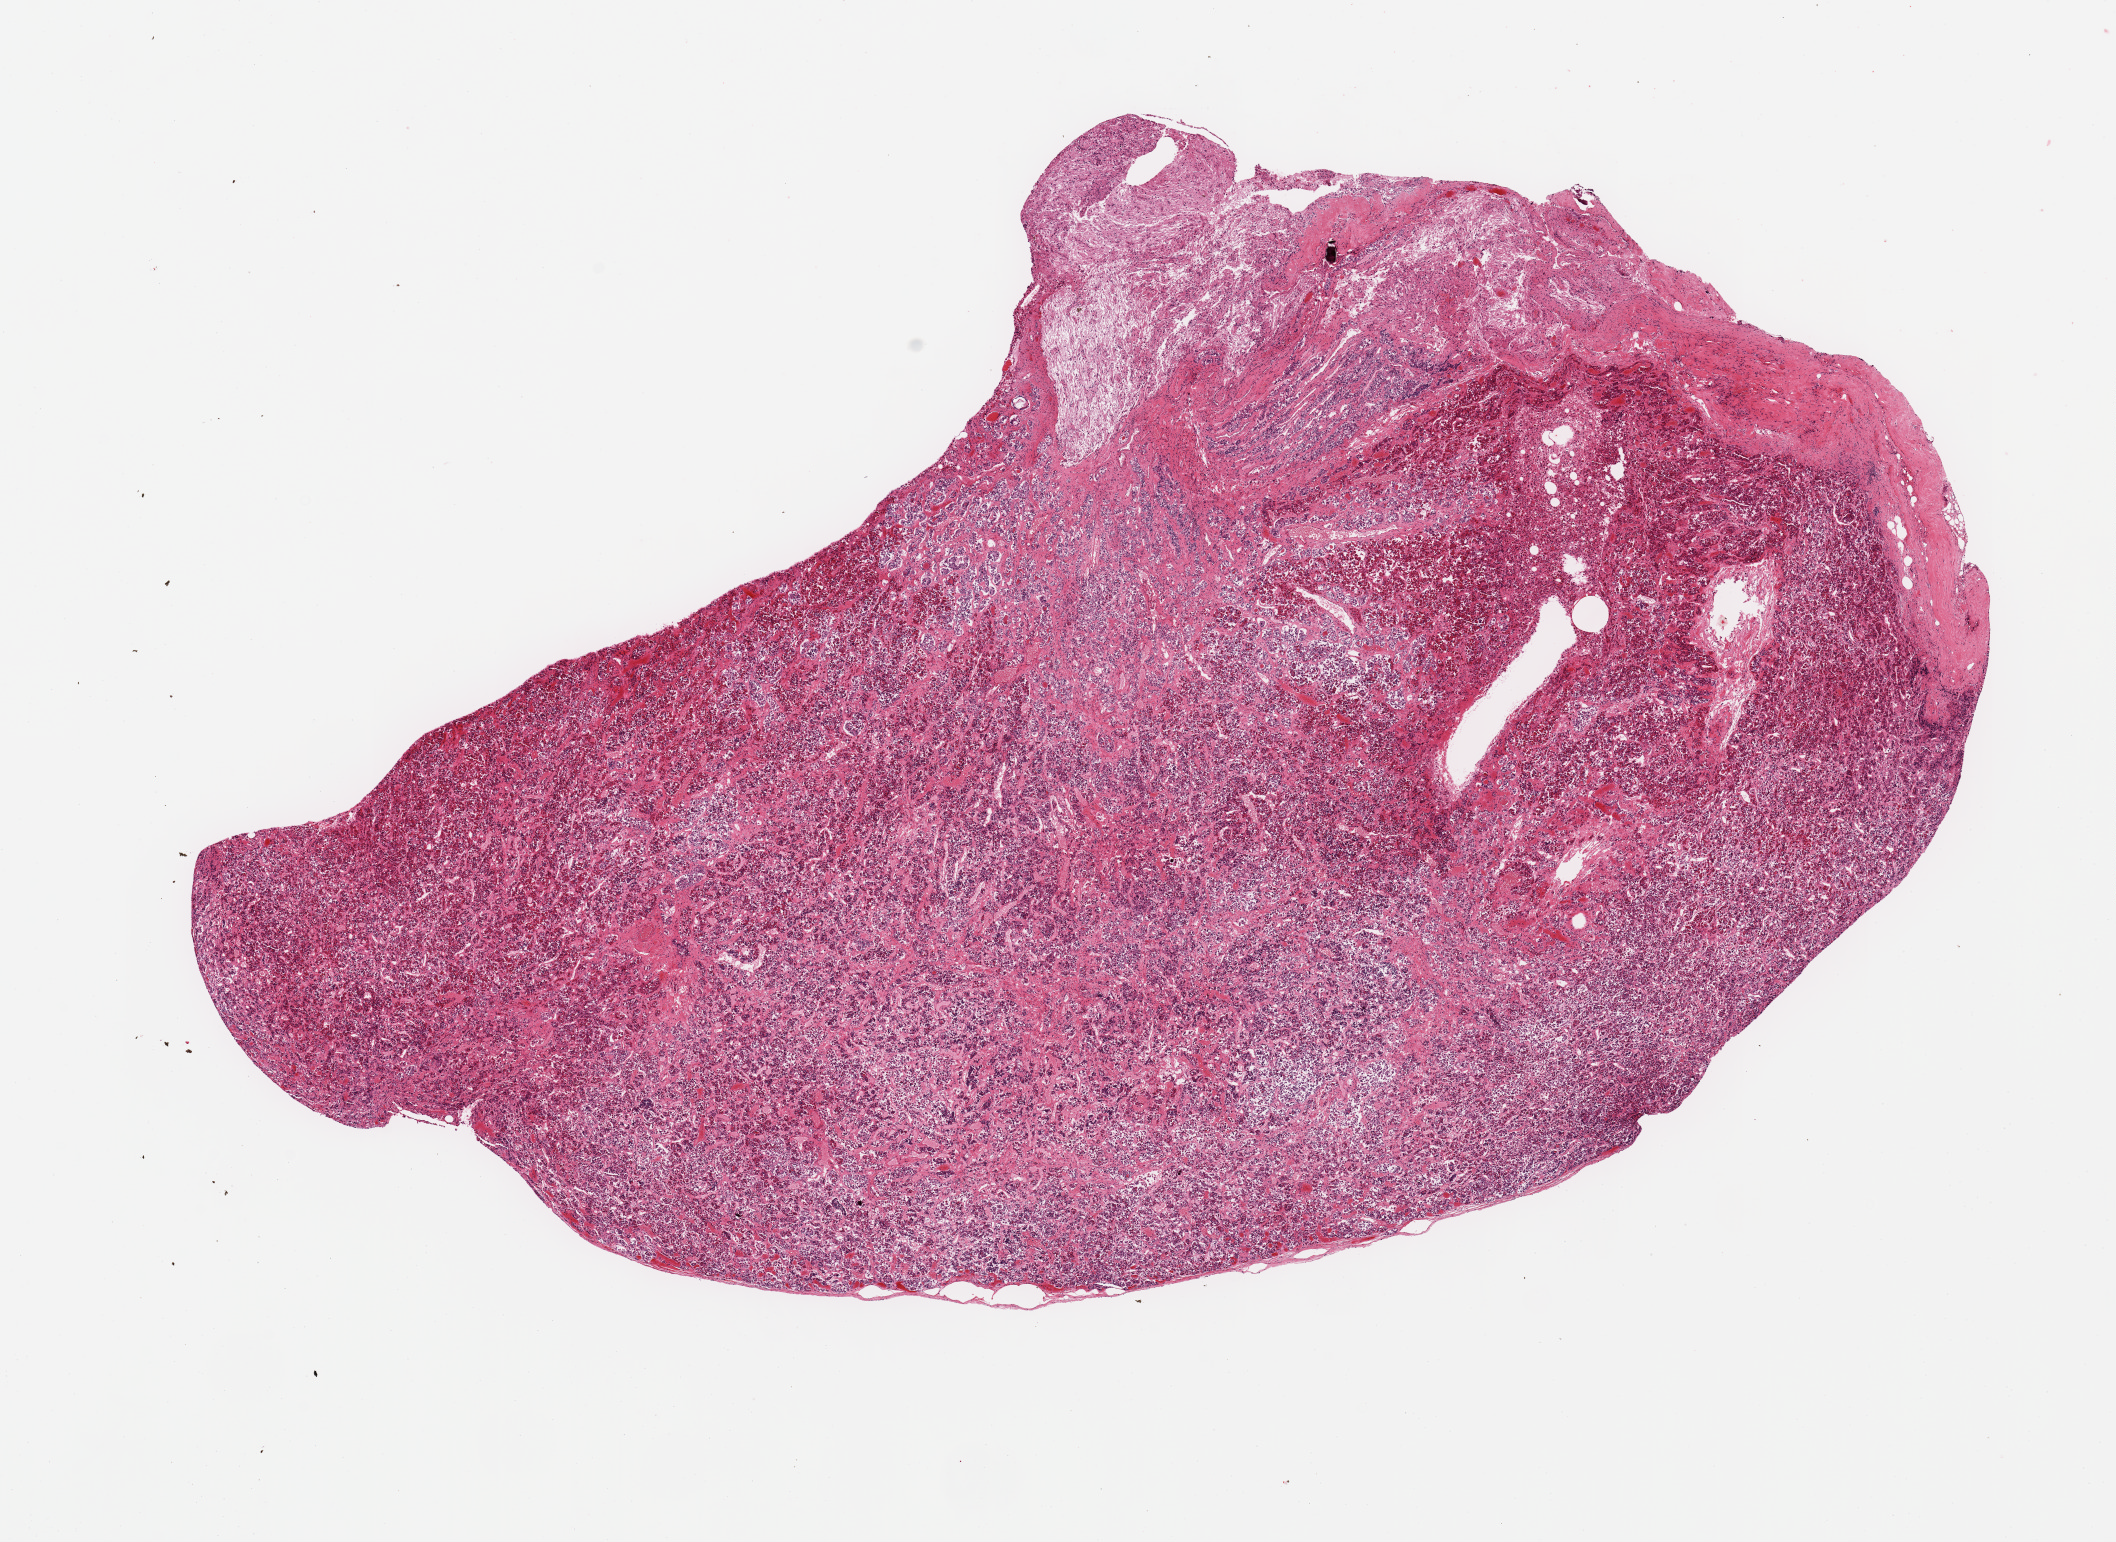
H&E whole-slide image, brightfield, a low-resolution overview of the entire scanned area, about 16.7 x 12.2 mm (slide scanned at 20x); PAXgene-fixed, paraffin-embedded tissue; target tissue: pituitary; tissue donor sample. Donor: male.
* pathologist's review note for this sample: 1 piece, ~4x3mm focus of neurohypophysis; rest is adenohypophysis